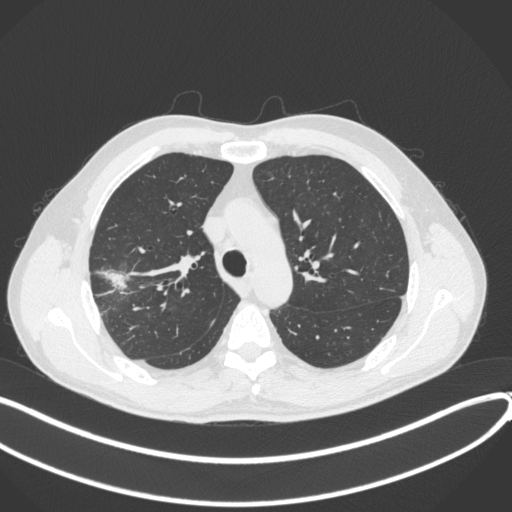
Chest CT, one axial slice. Slice 301 of 381 in the series (ordered by position). Lung window (W 1500 / L -600 HU). 1 mm slice thickness. 512 × 512 image matrix, field of view 400 × 400 mm. Patient: male, 62 years. From the clinical record (not read from this slice): clinical TNM (as recorded): T1c N0 M0; histopathological grade: G2-3.
Outlined on this slice (bounding box drawn by a radiologist):
- lung tumour (recorded histology: adenocarcinoma): box from (x=93, y=266) to (x=133, y=294) px